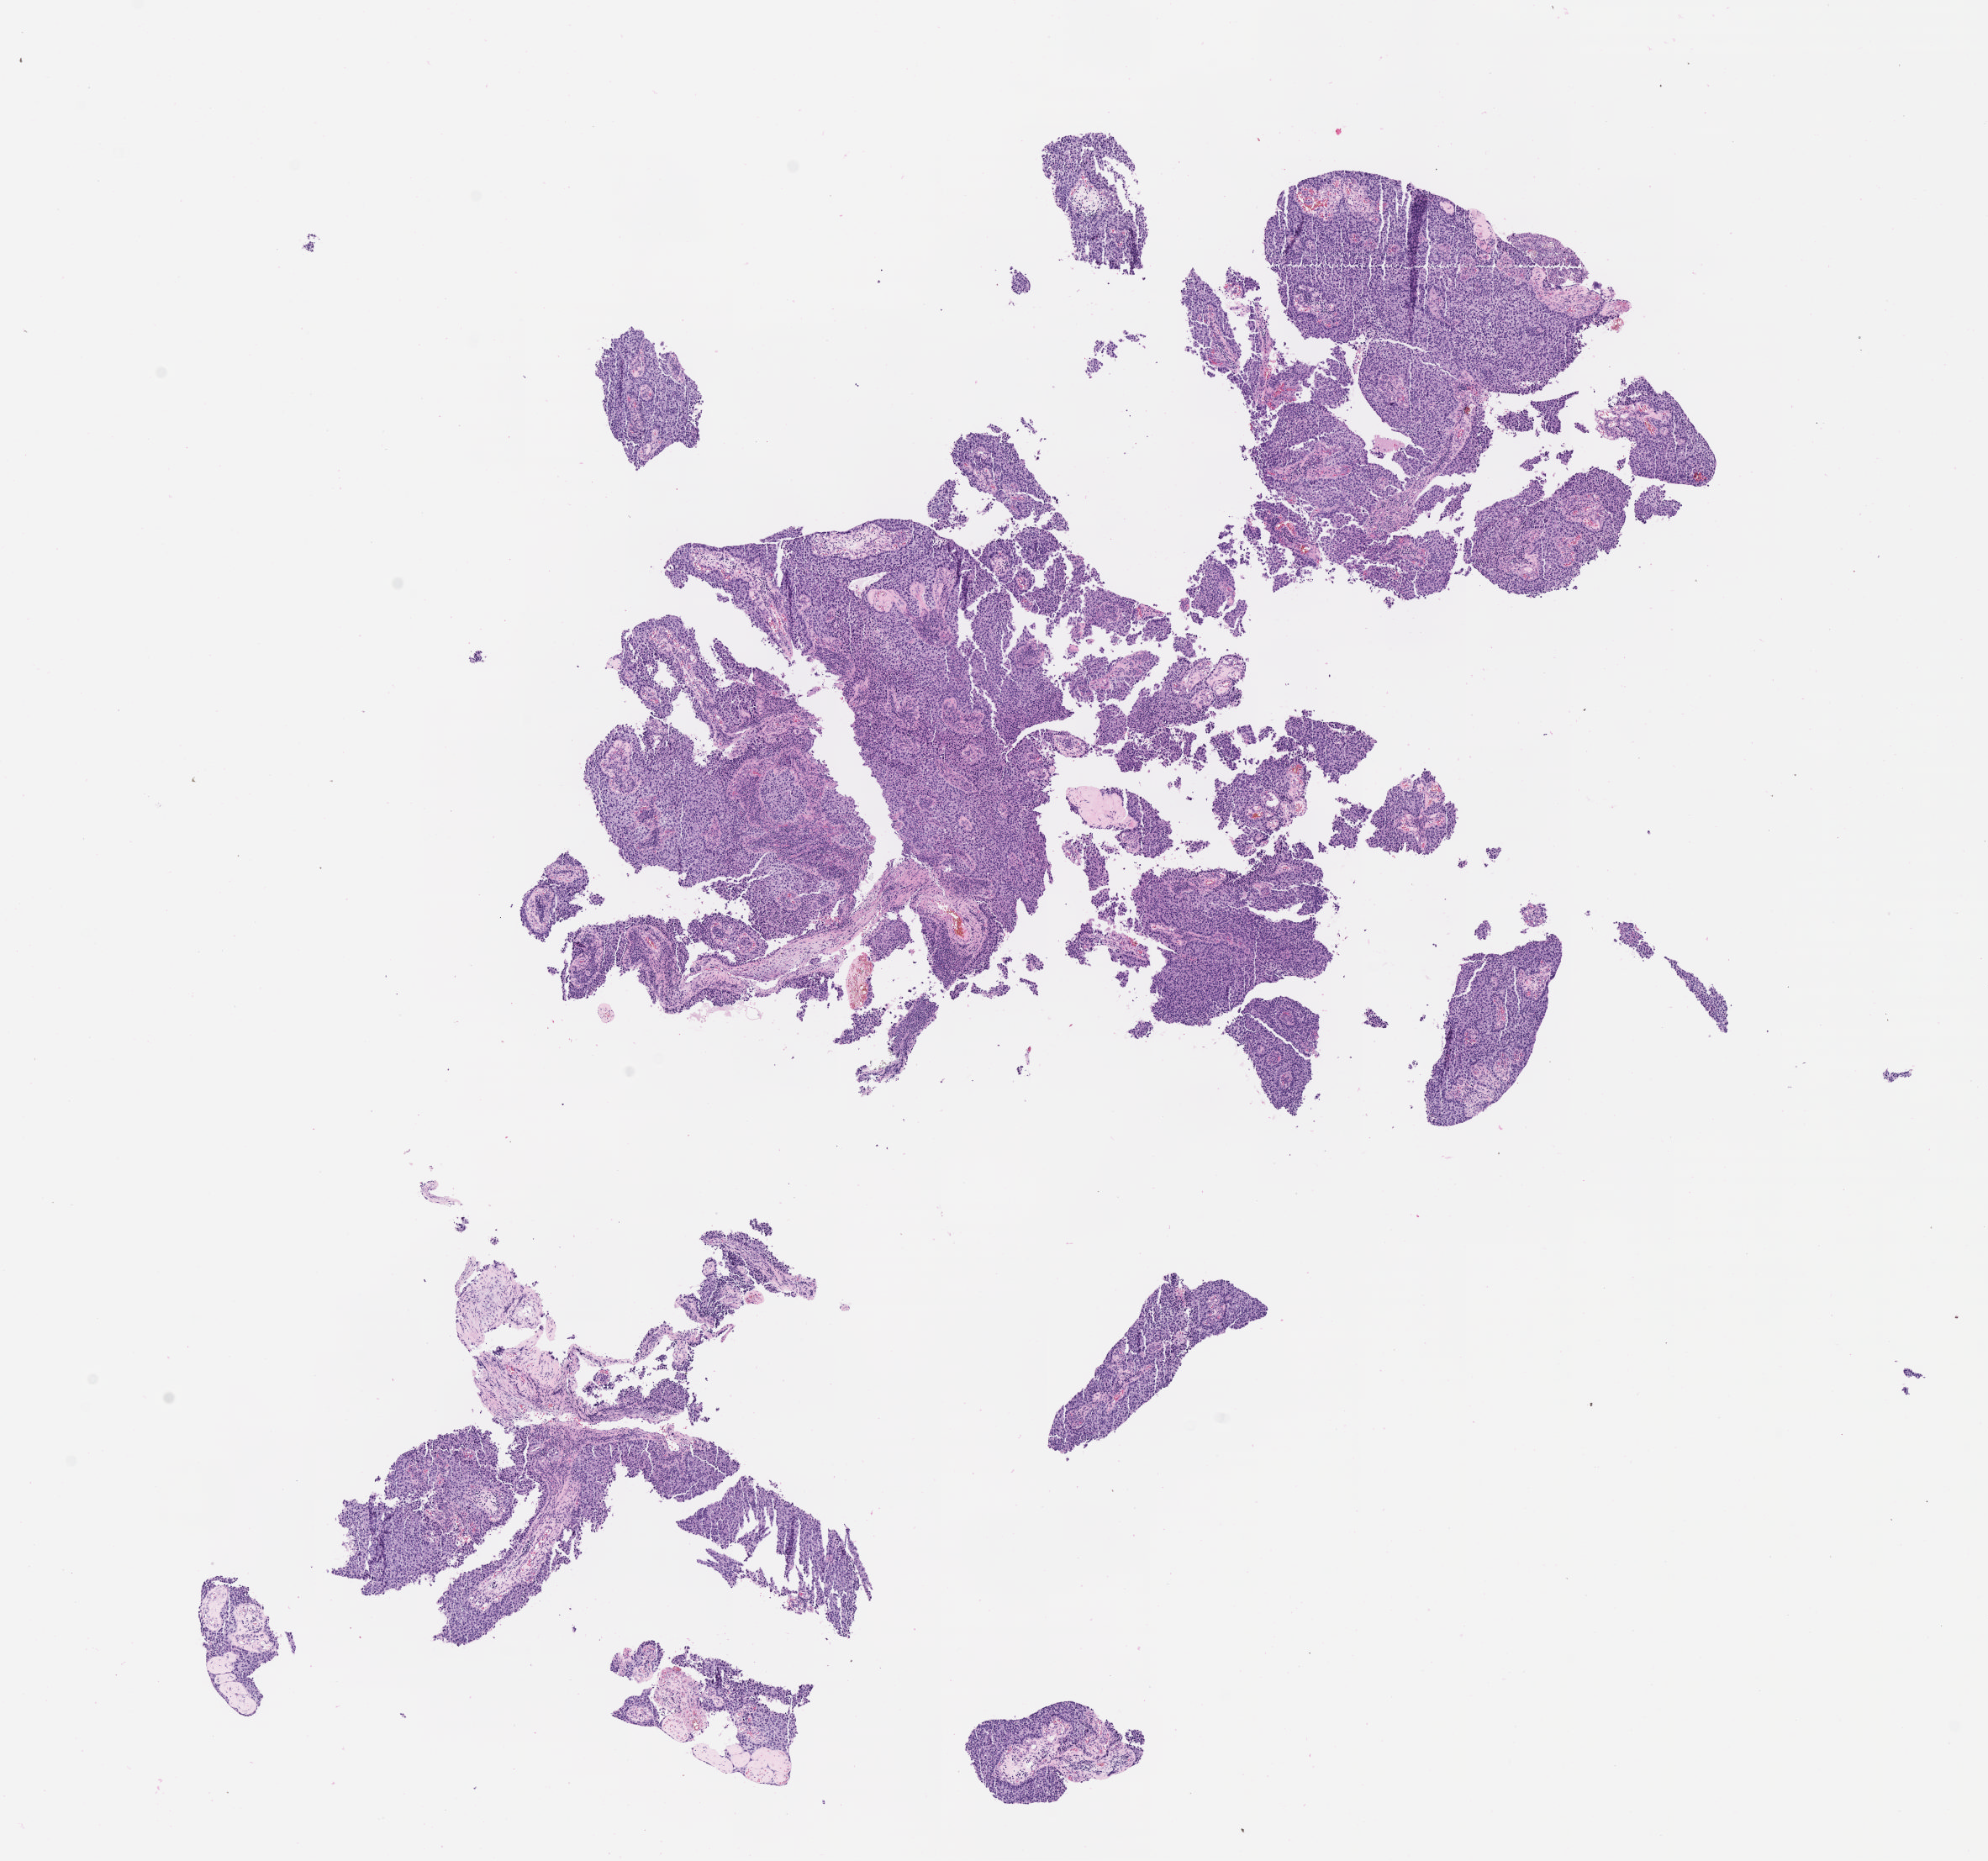
Haematoxylin and eosin whole-slide image, shown as a low-resolution overview of the whole scanned area (about 9.6 x 8.9 mm). Tumor tissue. Anatomic site: cervix. Female patient, 80 years old.
Histologic diagnosis: Squamous cell carcinoma, large cell, nonkeratinizing, NOS.